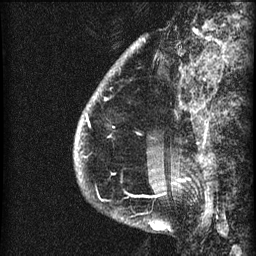
Breast MRI (dynamic contrast-enhanced), one sagittal slice. Slice 12 of 60 in the series (ordered by position). 3 images stored at this slice position (order not interpretable as contrast timing). 1.5 T. TE 4.2 ms, TR 22.7 ms. 2 mm slice thickness. 256 × 256 image matrix. Patient: female, 48 years. From the clinical record (not read from this slice): setting: breast cancer imaged before/during neoadjuvant chemotherapy; receptor status: triple-negative.
Structures marked on this image (semi-automatic segmentation, software-assisted and operator-edited):
- analysis volume of interest (the breast-tissue region the enhancement analysis was run in; not a lesion): box from (x=75, y=31) to (x=173, y=207) px
- tumour enhancement mask (voxels above the 90 % enhancement threshold inside the analysis volume of interest): (x=80, y=98)–(x=107, y=157)